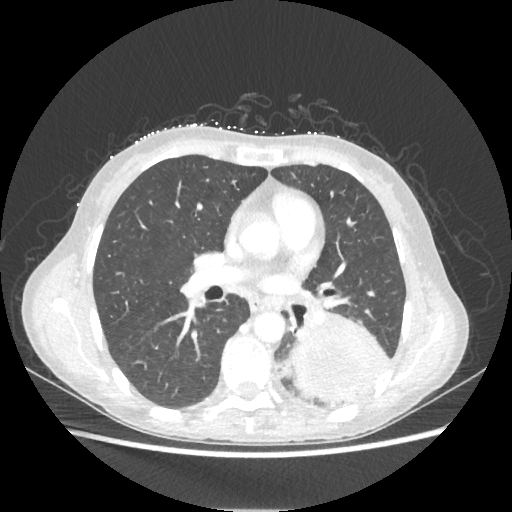
Chest CT, one axial slice. Slice 116 of 221 in the series (ordered by position). Reconstruction kernel STANDARD. Lung window (W 1500 / L -600 HU). 1.25 mm slice thickness. 512 × 512 image matrix. Female patient, age 53 years. Case-level facts recorded for this patient, not image findings: clinical TNM (as recorded): T3 N0 M0.
Structures marked on this image (bounding box drawn by a radiologist):
- lung tumour (recorded histology: adenocarcinoma): bounding box <290,308,393,405> (left, top, right, bottom; pixels)